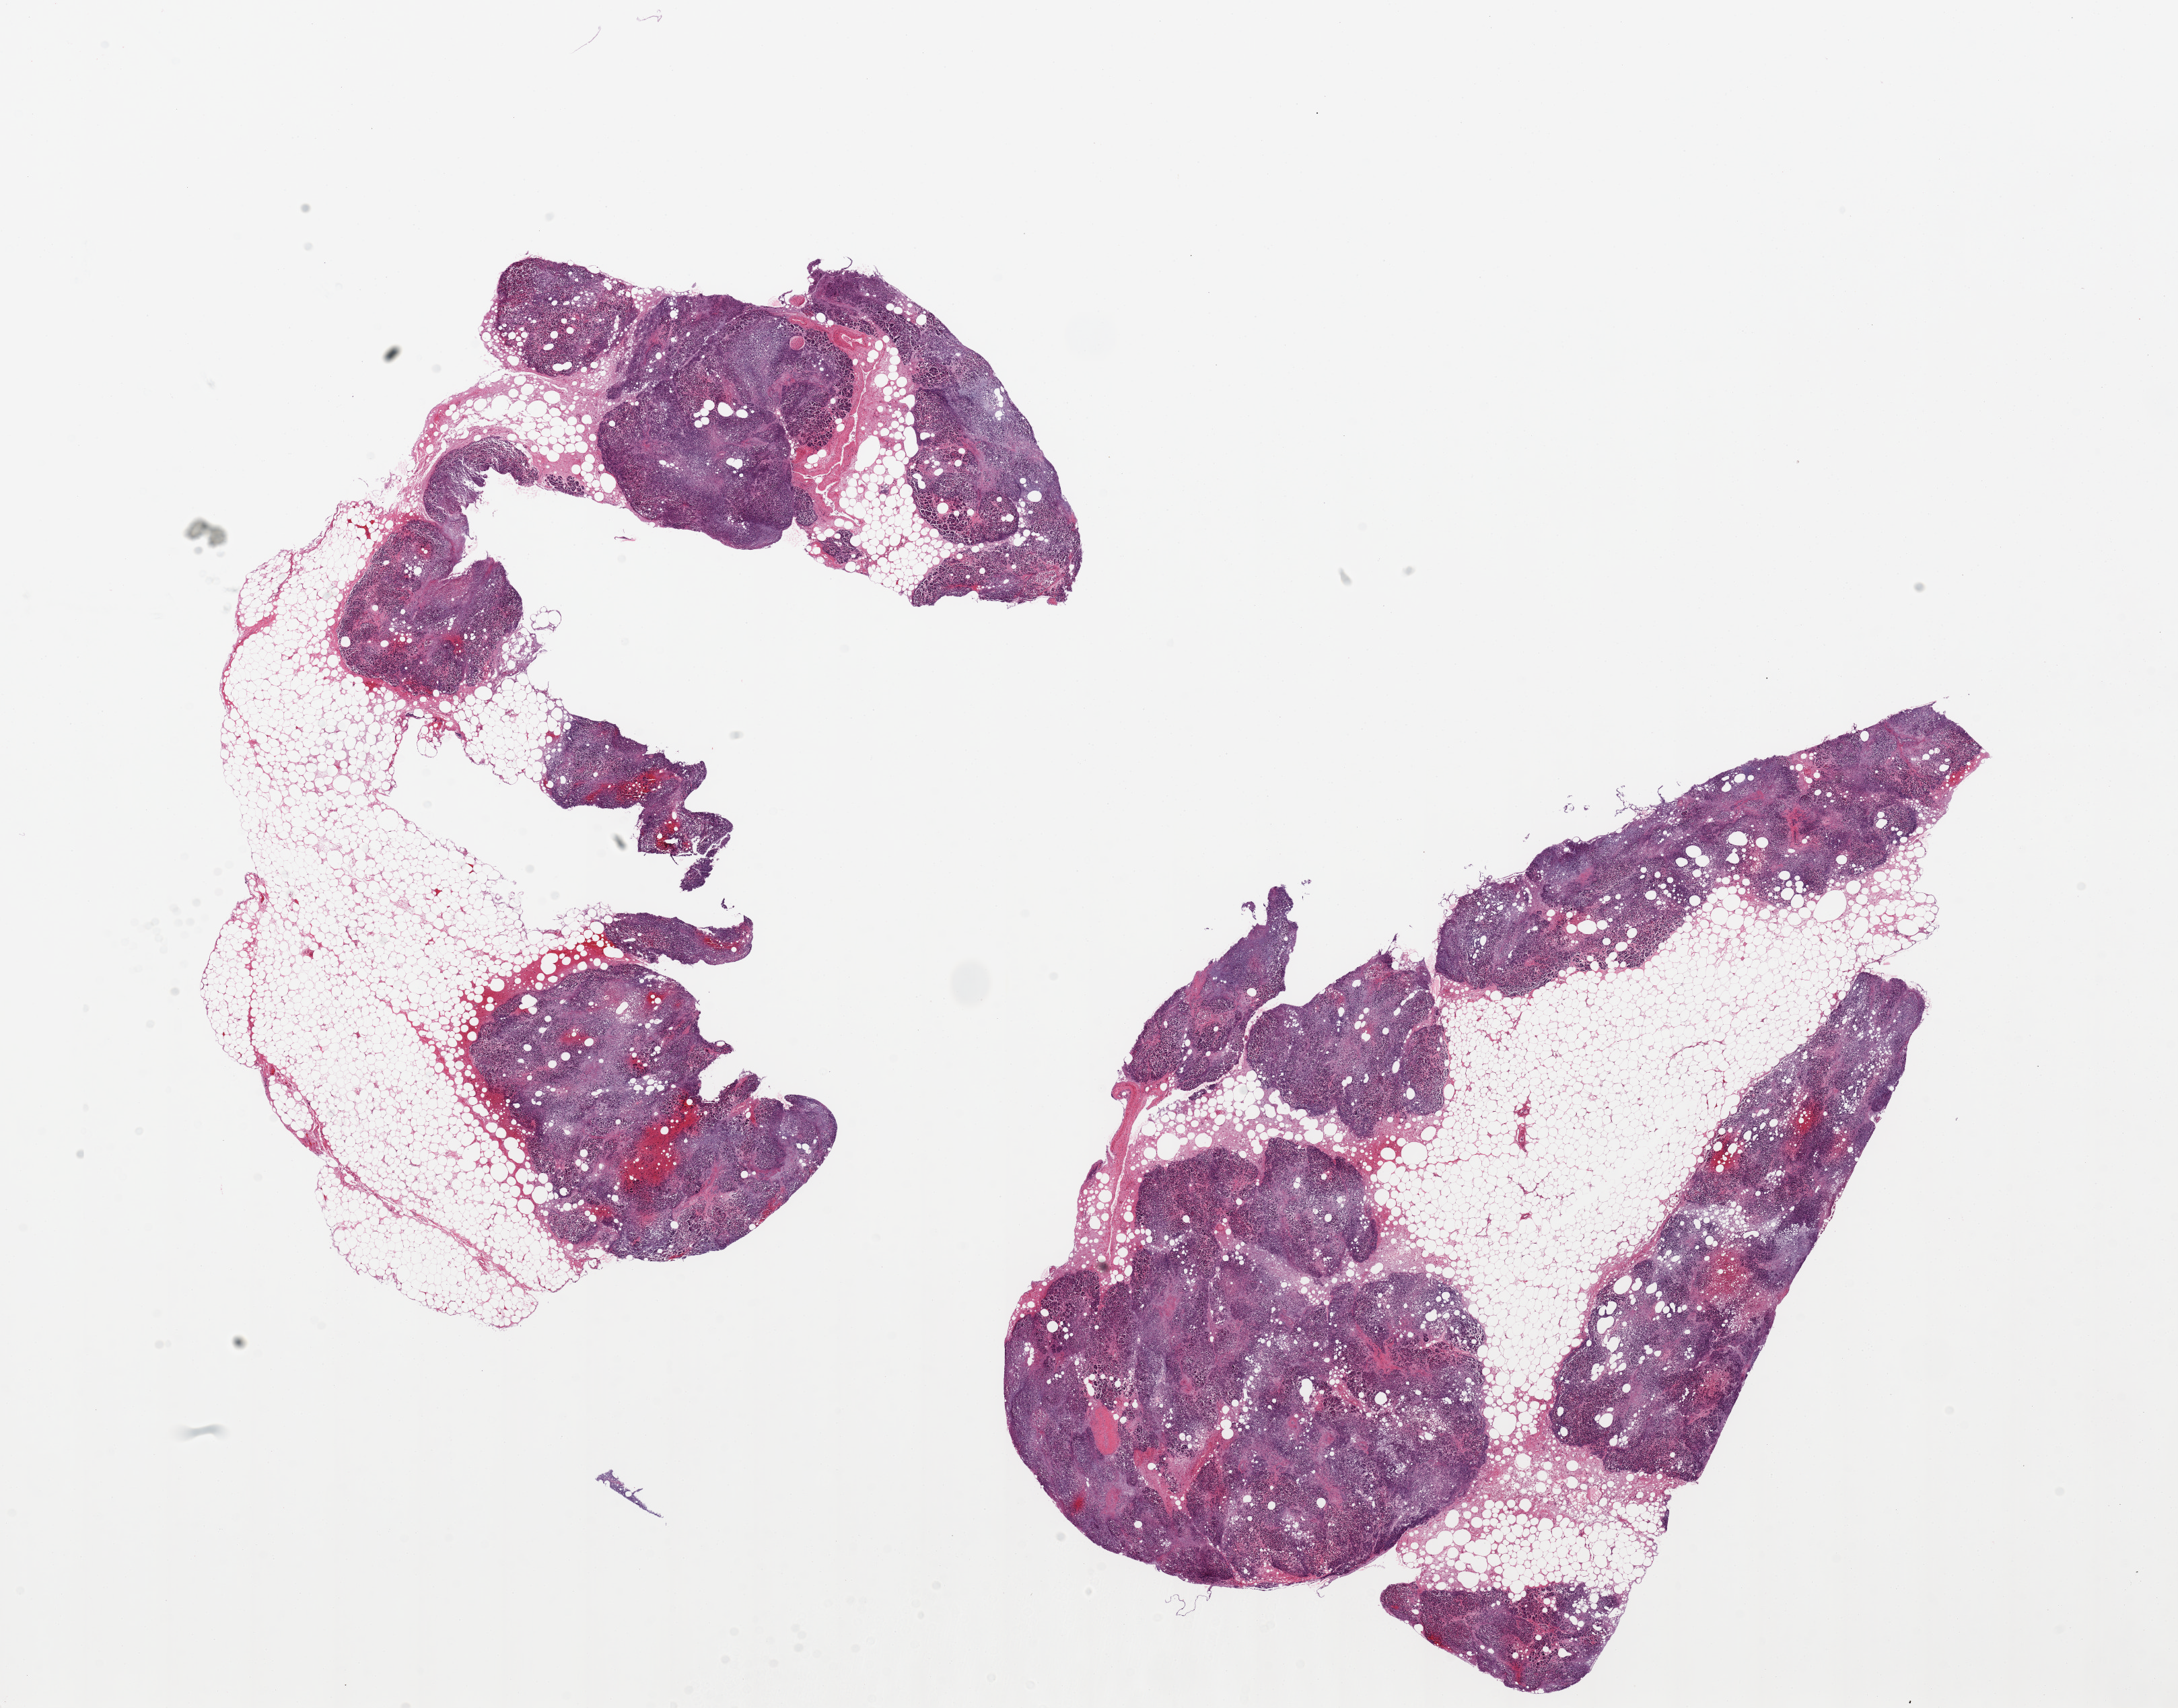
Digitized hematoxylin and eosin (H&E)-stained section, brightfield, low-resolution overview of the scanned area, about 25.6 x 20.1 mm; PAXgene-fixed paraffin-embedded (PFPE) section; target tissue: pancreas; donor tissue sample.
Review note (as recorded): 2 pieces, fat from 30 to 50%, severe autolysis.